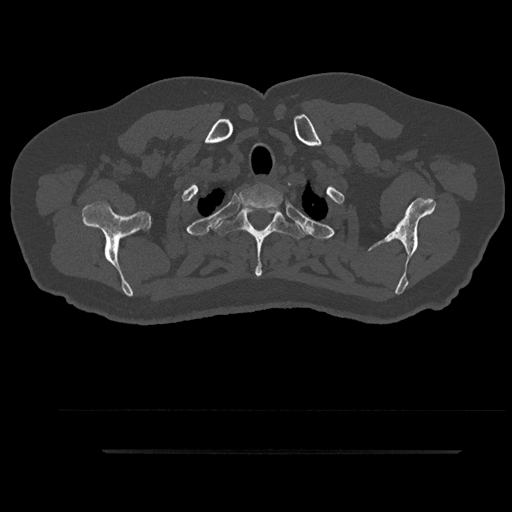
CT including the spine, one axial slice; slice 770 of 797 in the series (ordered by position); reconstruction kernel Br40s/3; bone window (W 1800 / L 400 HU); 512 × 512 image matrix, field of view 432 × 432 mm. Male patient, age 63 years. From the clinical record (not read from this slice): primary cancer: renal; vertebrae with lytic lesions (as recorded): T8.
Annotated regions visible in this slice (semi-automatically segmented with operator editing):
- T1 vertebra: bounding box (x1, y1, x2, y2) in pixels: (237, 185, 282, 221)
- T2 vertebra: (213, 206, 306, 277)